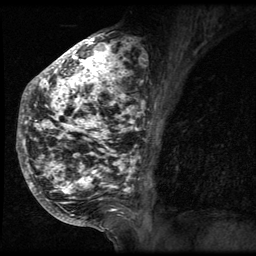
Breast MRI (dynamic contrast-enhanced), one sagittal slice; slice 29 of 64 in the series (ordered by position); 3 images stored at this slice position (order not interpretable as contrast timing); 1.5 T; TE 4.2 ms, TR 9 ms; 2.5 mm slice thickness; 256 × 256 image matrix, field of view 180 × 180 mm. Patient: female, 50 years. From the clinical record (not read from this slice): setting: breast cancer imaged before/during neoadjuvant chemotherapy; receptor status: triple-negative.
Structures marked on this image (semi-automatic segmentation, software-assisted and operator-edited):
- analysis volume of interest (the breast-tissue region the enhancement analysis was run in; not a lesion): bounding box [x1, y1, x2, y2] px = [24, 39, 144, 212]
- tumour enhancement mask (voxels above the 140 % enhancement threshold inside the analysis volume of interest): [24, 39, 144, 211]